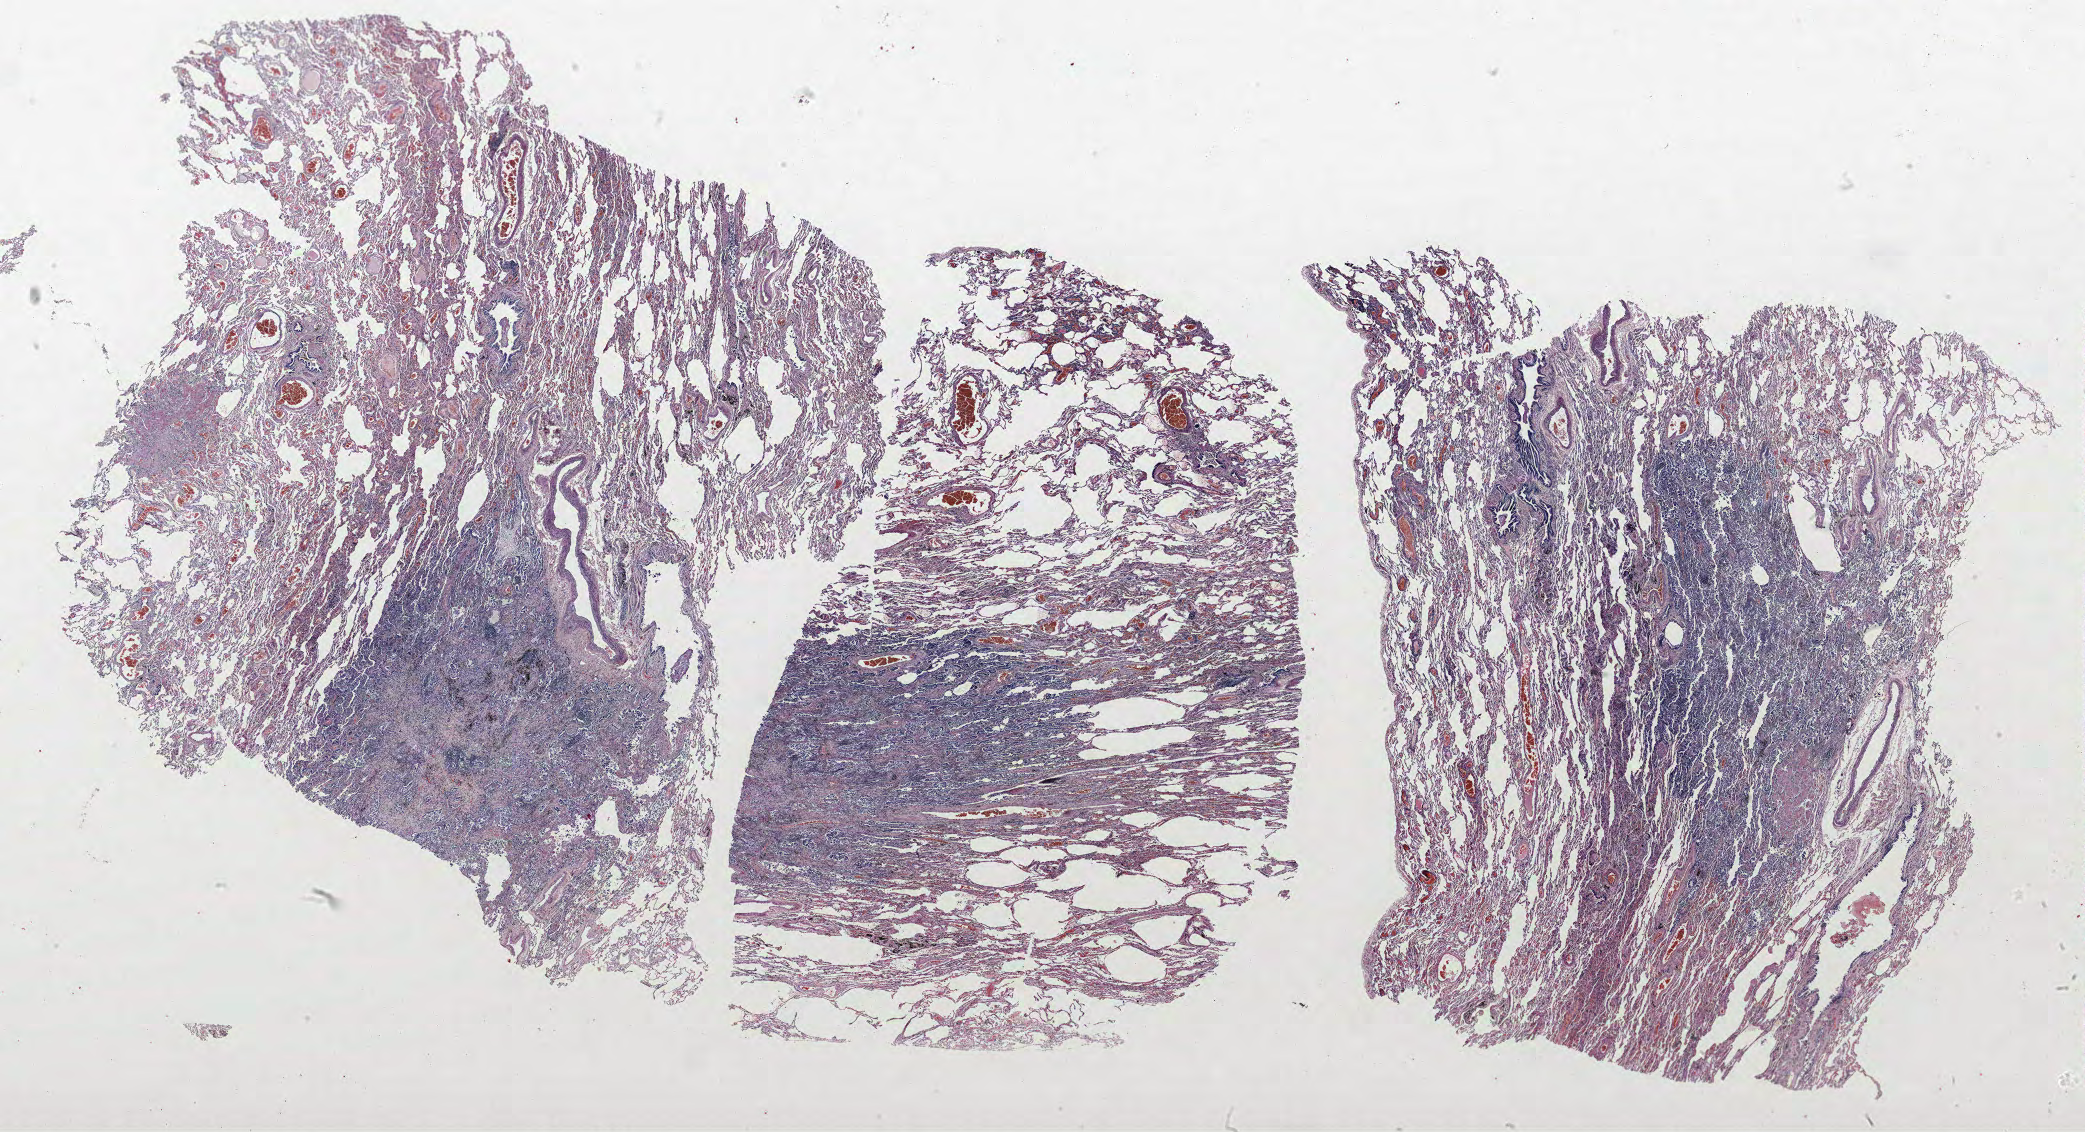
H&E whole-slide image, a low-resolution overview of the entire scanned area, about 33.4 x 18.1 mm (acquisition: 40x scan), formalin-fixed paraffin-embedded (FFPE) section, lung. Male patient, aged 66 at enrolment.
- stage (AJCC 6th edition): IA
- participant's lung-cancer diagnosis: Squamous cell carcinoma, NOS
- tumour size (pathology): 23 mm
- primary tumour location (clinical record): left upper lobe
- note: participant had 2 primary lung cancers recorded; fields above describe the first